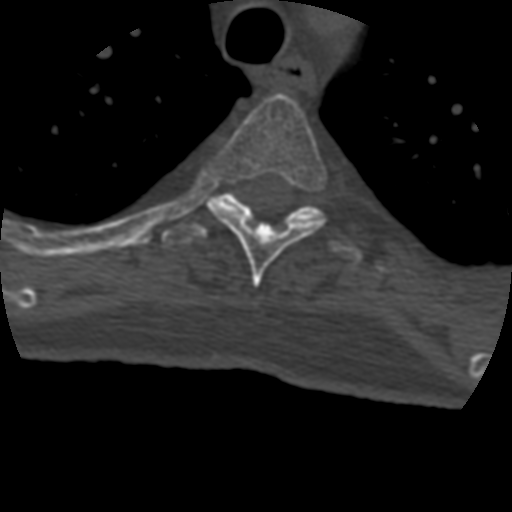
CT including the spine, one axial slice. Position 332 of 399 along the scan axis. Reconstruction kernel STANDARD. Bone window (W 1800 / L 400 HU). 1.25 mm slice thickness. 512 × 512 image matrix, field of view 160 × 160 mm. Patient age 69 years. From the clinical record (not read from this slice): primary cancer: prostate.
Structures marked on this image (semi-automatically segmented with operator editing):
- T4 vertebra: bounding box [x1, y1, x2, y2] px = [207, 94, 328, 288]
- T5 vertebra: [161, 191, 363, 264]